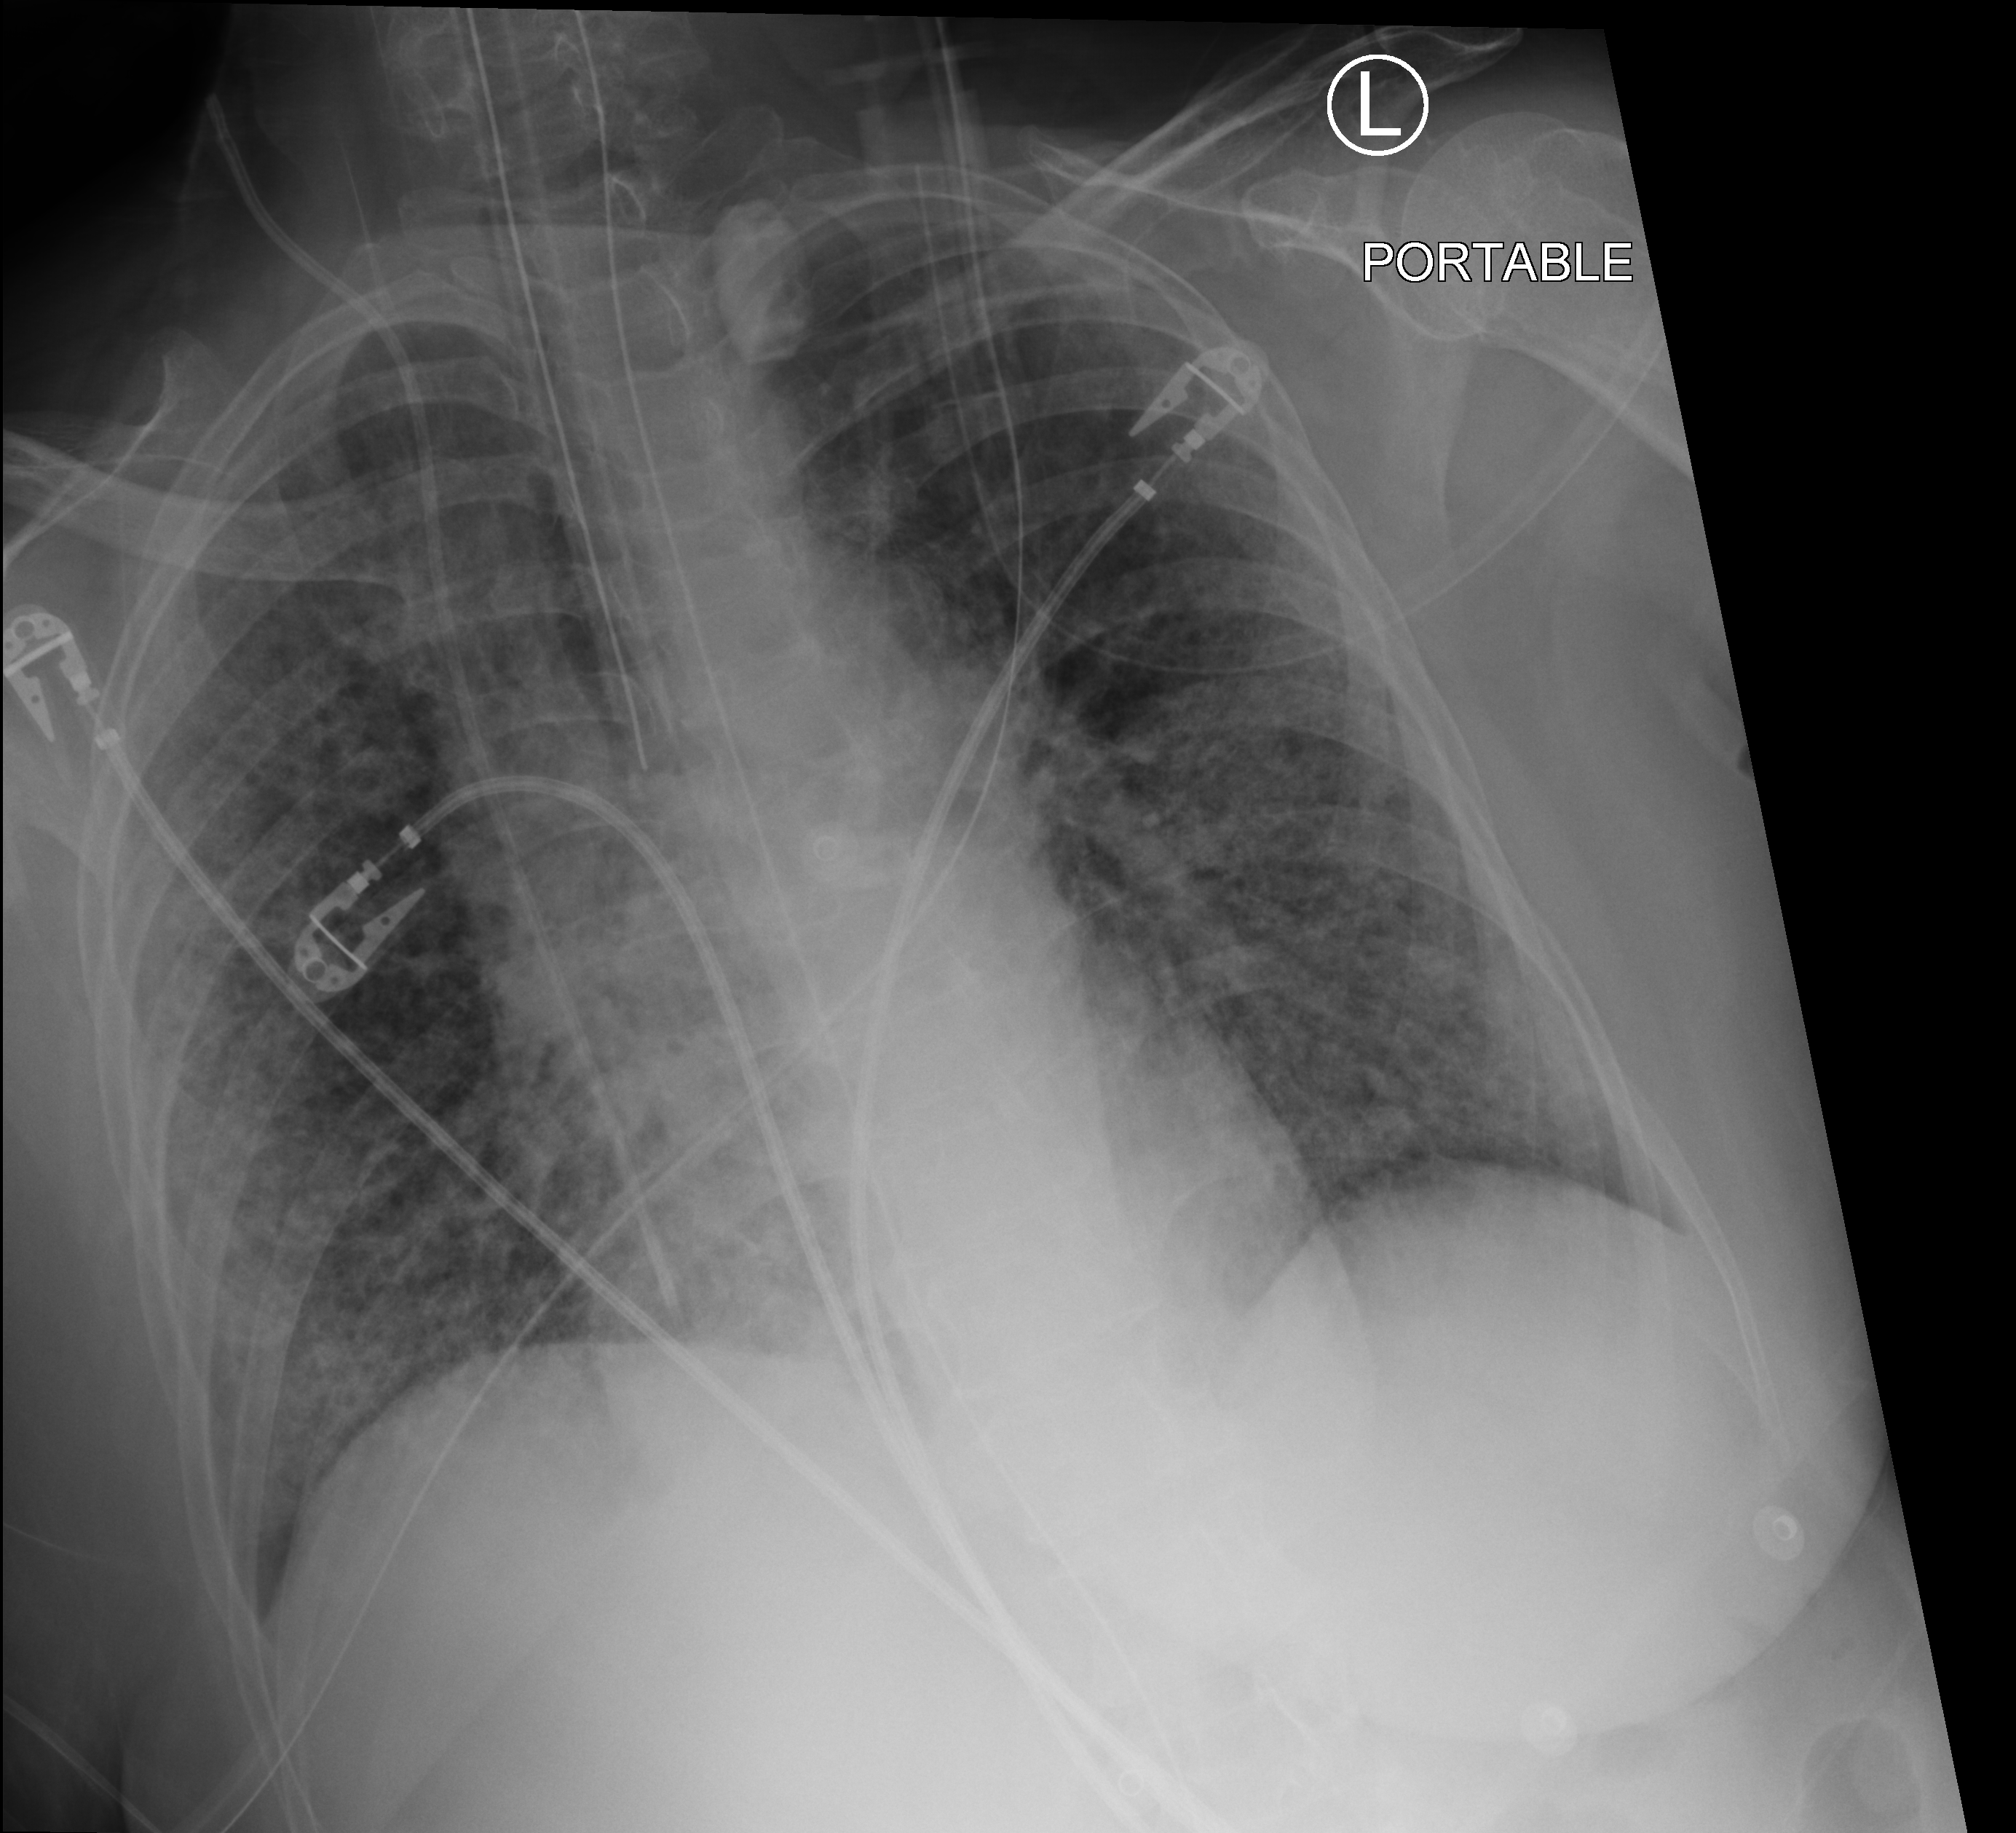
Bedside chest radiograph (computed radiography), anteroposterior (AP) projection. Female patient hospitalised with COVID-19, age 60–74 years.
Hospital-stay facts (about this admission, not read from this image; timing relative to this image not recorded): admitted to intensive care during this hospital stay: yes; COPD (admission record): no; length of hospital stay: 14 days.